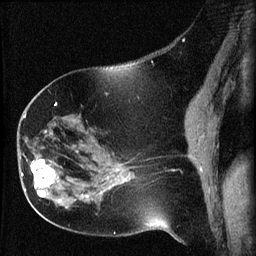
Breast MRI (dynamic contrast-enhanced), one sagittal slice. Slice 28 of 60 in the series (ordered by position). Dynamic contrast-enhanced series, image 2 of 3 at this slice position (ordered by acquisition). 1.5 T. TE 4.2 ms, TR 8.2 ms. 256 × 256 image matrix, field of view 180 × 180 mm. Patient: female, 63 years.
Annotated regions visible in this slice (semi-automatic segmentation, software-assisted and operator-edited):
- analysis volume of interest (the breast-tissue region the enhancement analysis was run in; not a lesion): bounding box (x1, y1, x2, y2) in pixels: (22, 156, 64, 202)
- tumour enhancement mask (voxels above the 70 % enhancement threshold inside the analysis volume of interest): (22, 159, 60, 202)